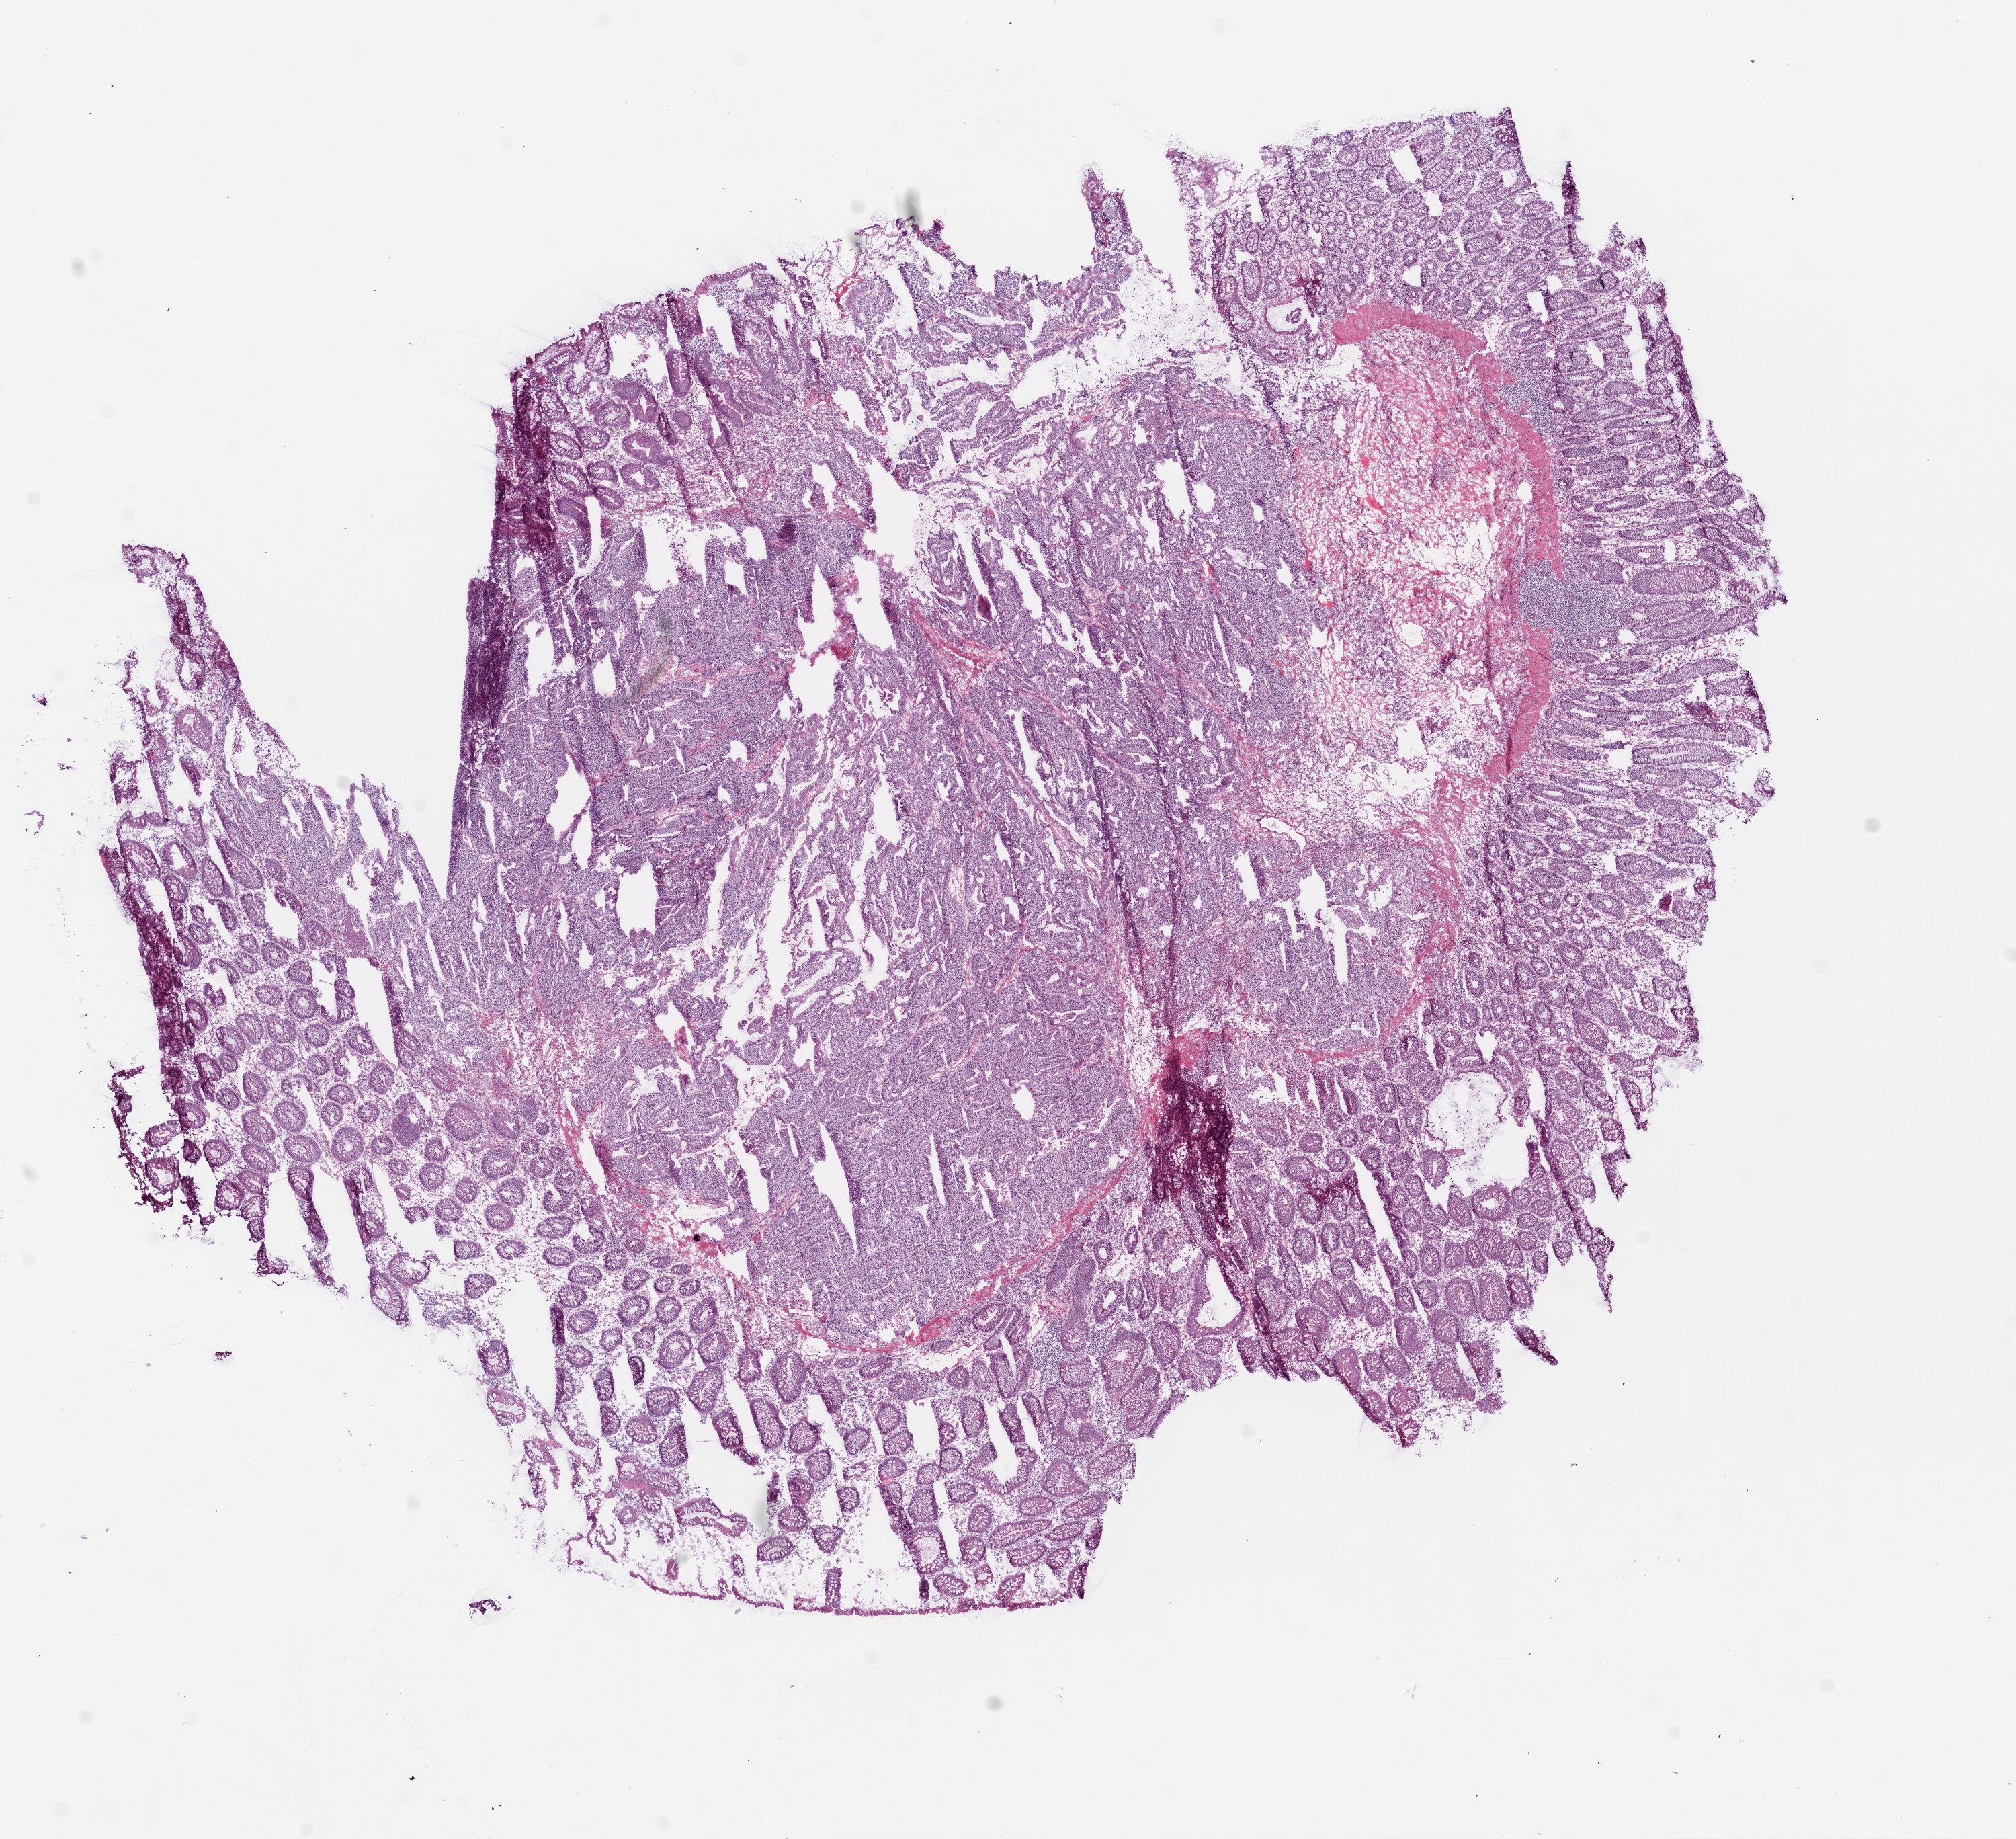
Digitized Hematoxylin and eosin (H&E) stained tissue section (whole slide) — shown as a low-resolution overview of the whole scanned area (about 12.0 x 11.0 mm, slide scanned at 20x), frozen section from the bottom of the tissue portion, colon, primary tumour sample. Male patient. Pathologist review of this section (percent, as recorded): tumour cells 60%, tumour nuclei 70%, normal cells 30%, stromal cells 10%, necrosis 0%.
* lymph nodes positive (case pathology): 2 of 28 examined
* AJCC pathologic stage: IIIB
* diagnosis: Adenocarcinoma, NOS (ascending colon)